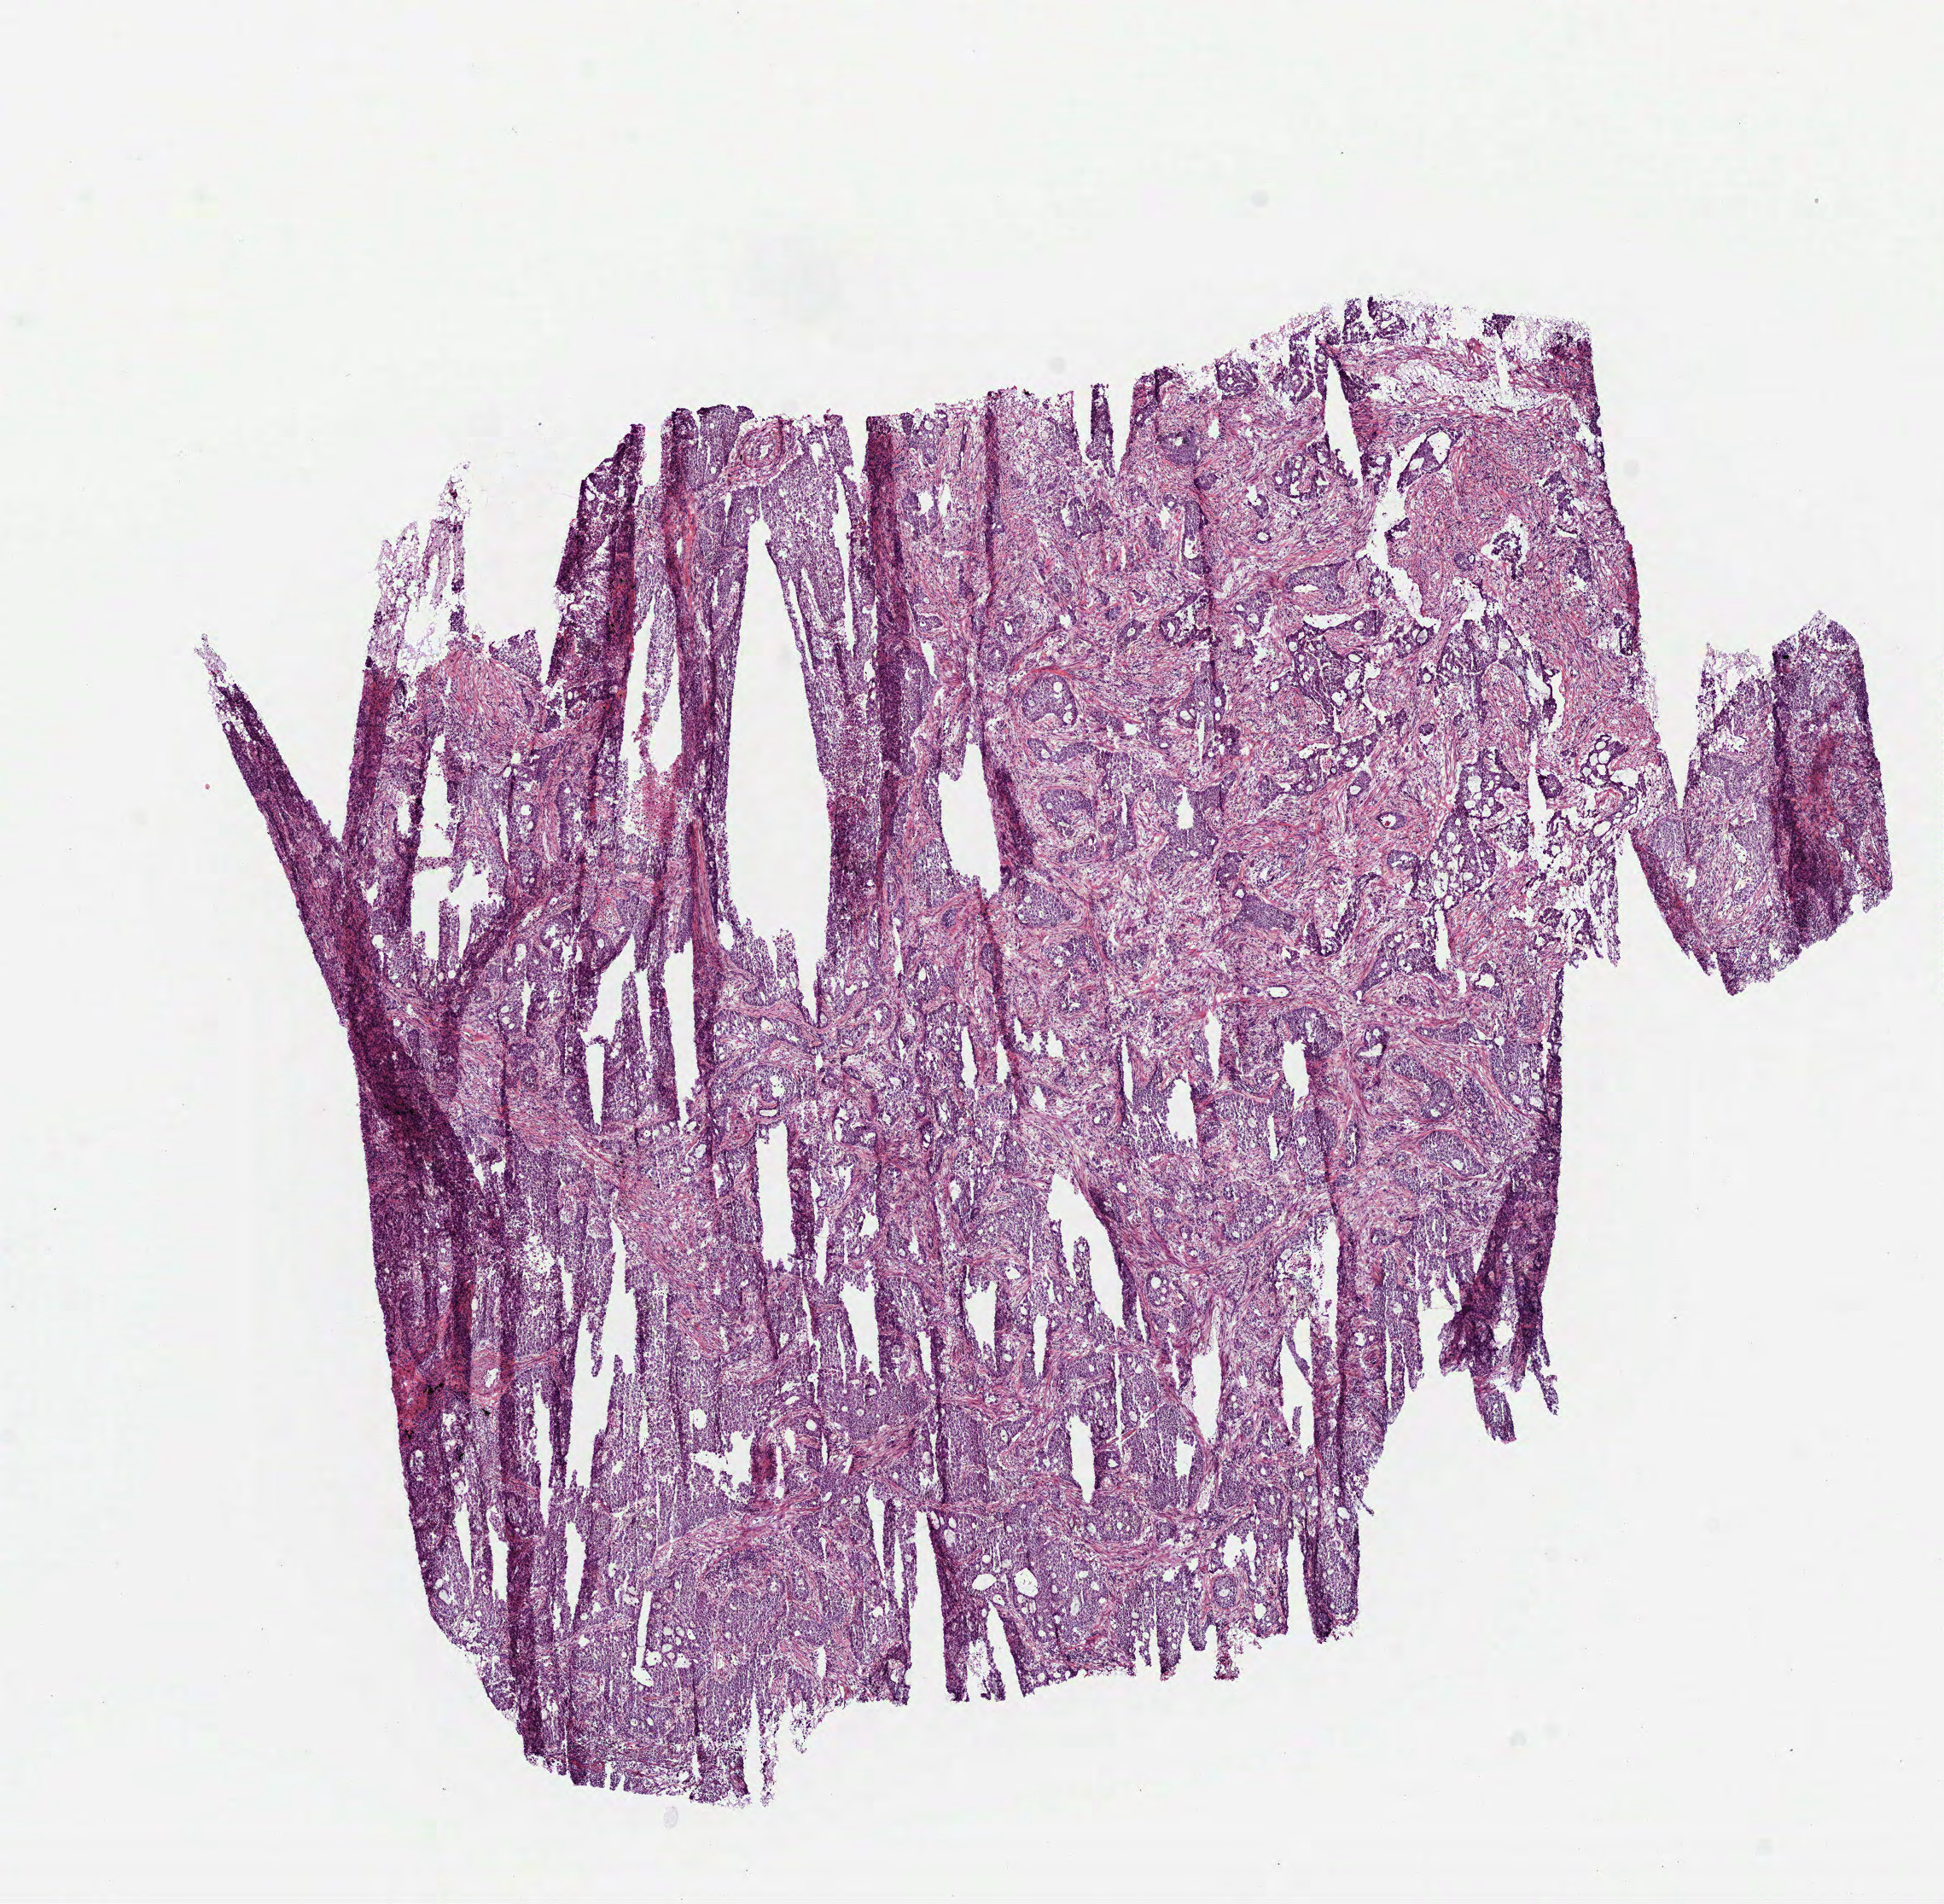
H&E whole-slide image, whole scanned area (about 9.2 x 9.0 mm, acquisition: 40x scan) shown as a low-resolution overview; frozen section from the bottom of the tissue portion; lung, primary tumour sample. Patient sex: male. Slide review estimates, as recorded: tumour cells 77%, tumour nuclei 70%, normal cells 0%, stromal cells 15%, necrosis 8%.
Pathologic diagnosis: Adenocarcinoma, NOS (lower lobe, lung). AJCC pathologic stage: IB (6th edition). Laterality: left.